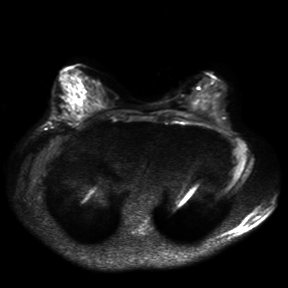
Breast MRI, one axial slice; position 15 of 30 along the scan axis; diffusion-weighted series; image 2 of 4 stored at this slice position (different b-values; order by instance number); 3 T; 4 mm slice thickness; 288 × 288 image matrix, field of view 360 × 360 mm. Female patient.
Annotated regions visible in this slice (outlined manually by an expert reader):
- tumour on diffusion-weighted imaging: bounding box (x1, y1, x2, y2) in pixels: (65, 114, 76, 122)